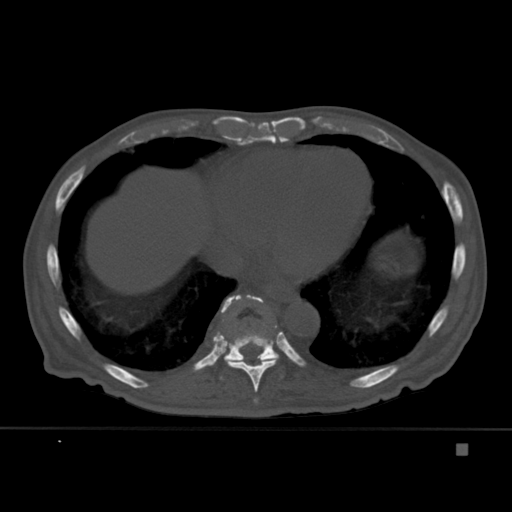
CT including the spine, one axial slice. Bone window (W 1800 / L 400 HU). 1.5 mm slice thickness. 512 × 512 image matrix, field of view 378 × 378 mm. Patient: male, 75 years. From the clinical record (not read from this slice): primary cancer: prostate.
Outlined on this slice (semi-automatically segmented with operator editing):
- T10 vertebra: bounding box [x1, y1, x2, y2] px = [220, 295, 282, 380]
- T9 vertebra: [215, 295, 282, 403]